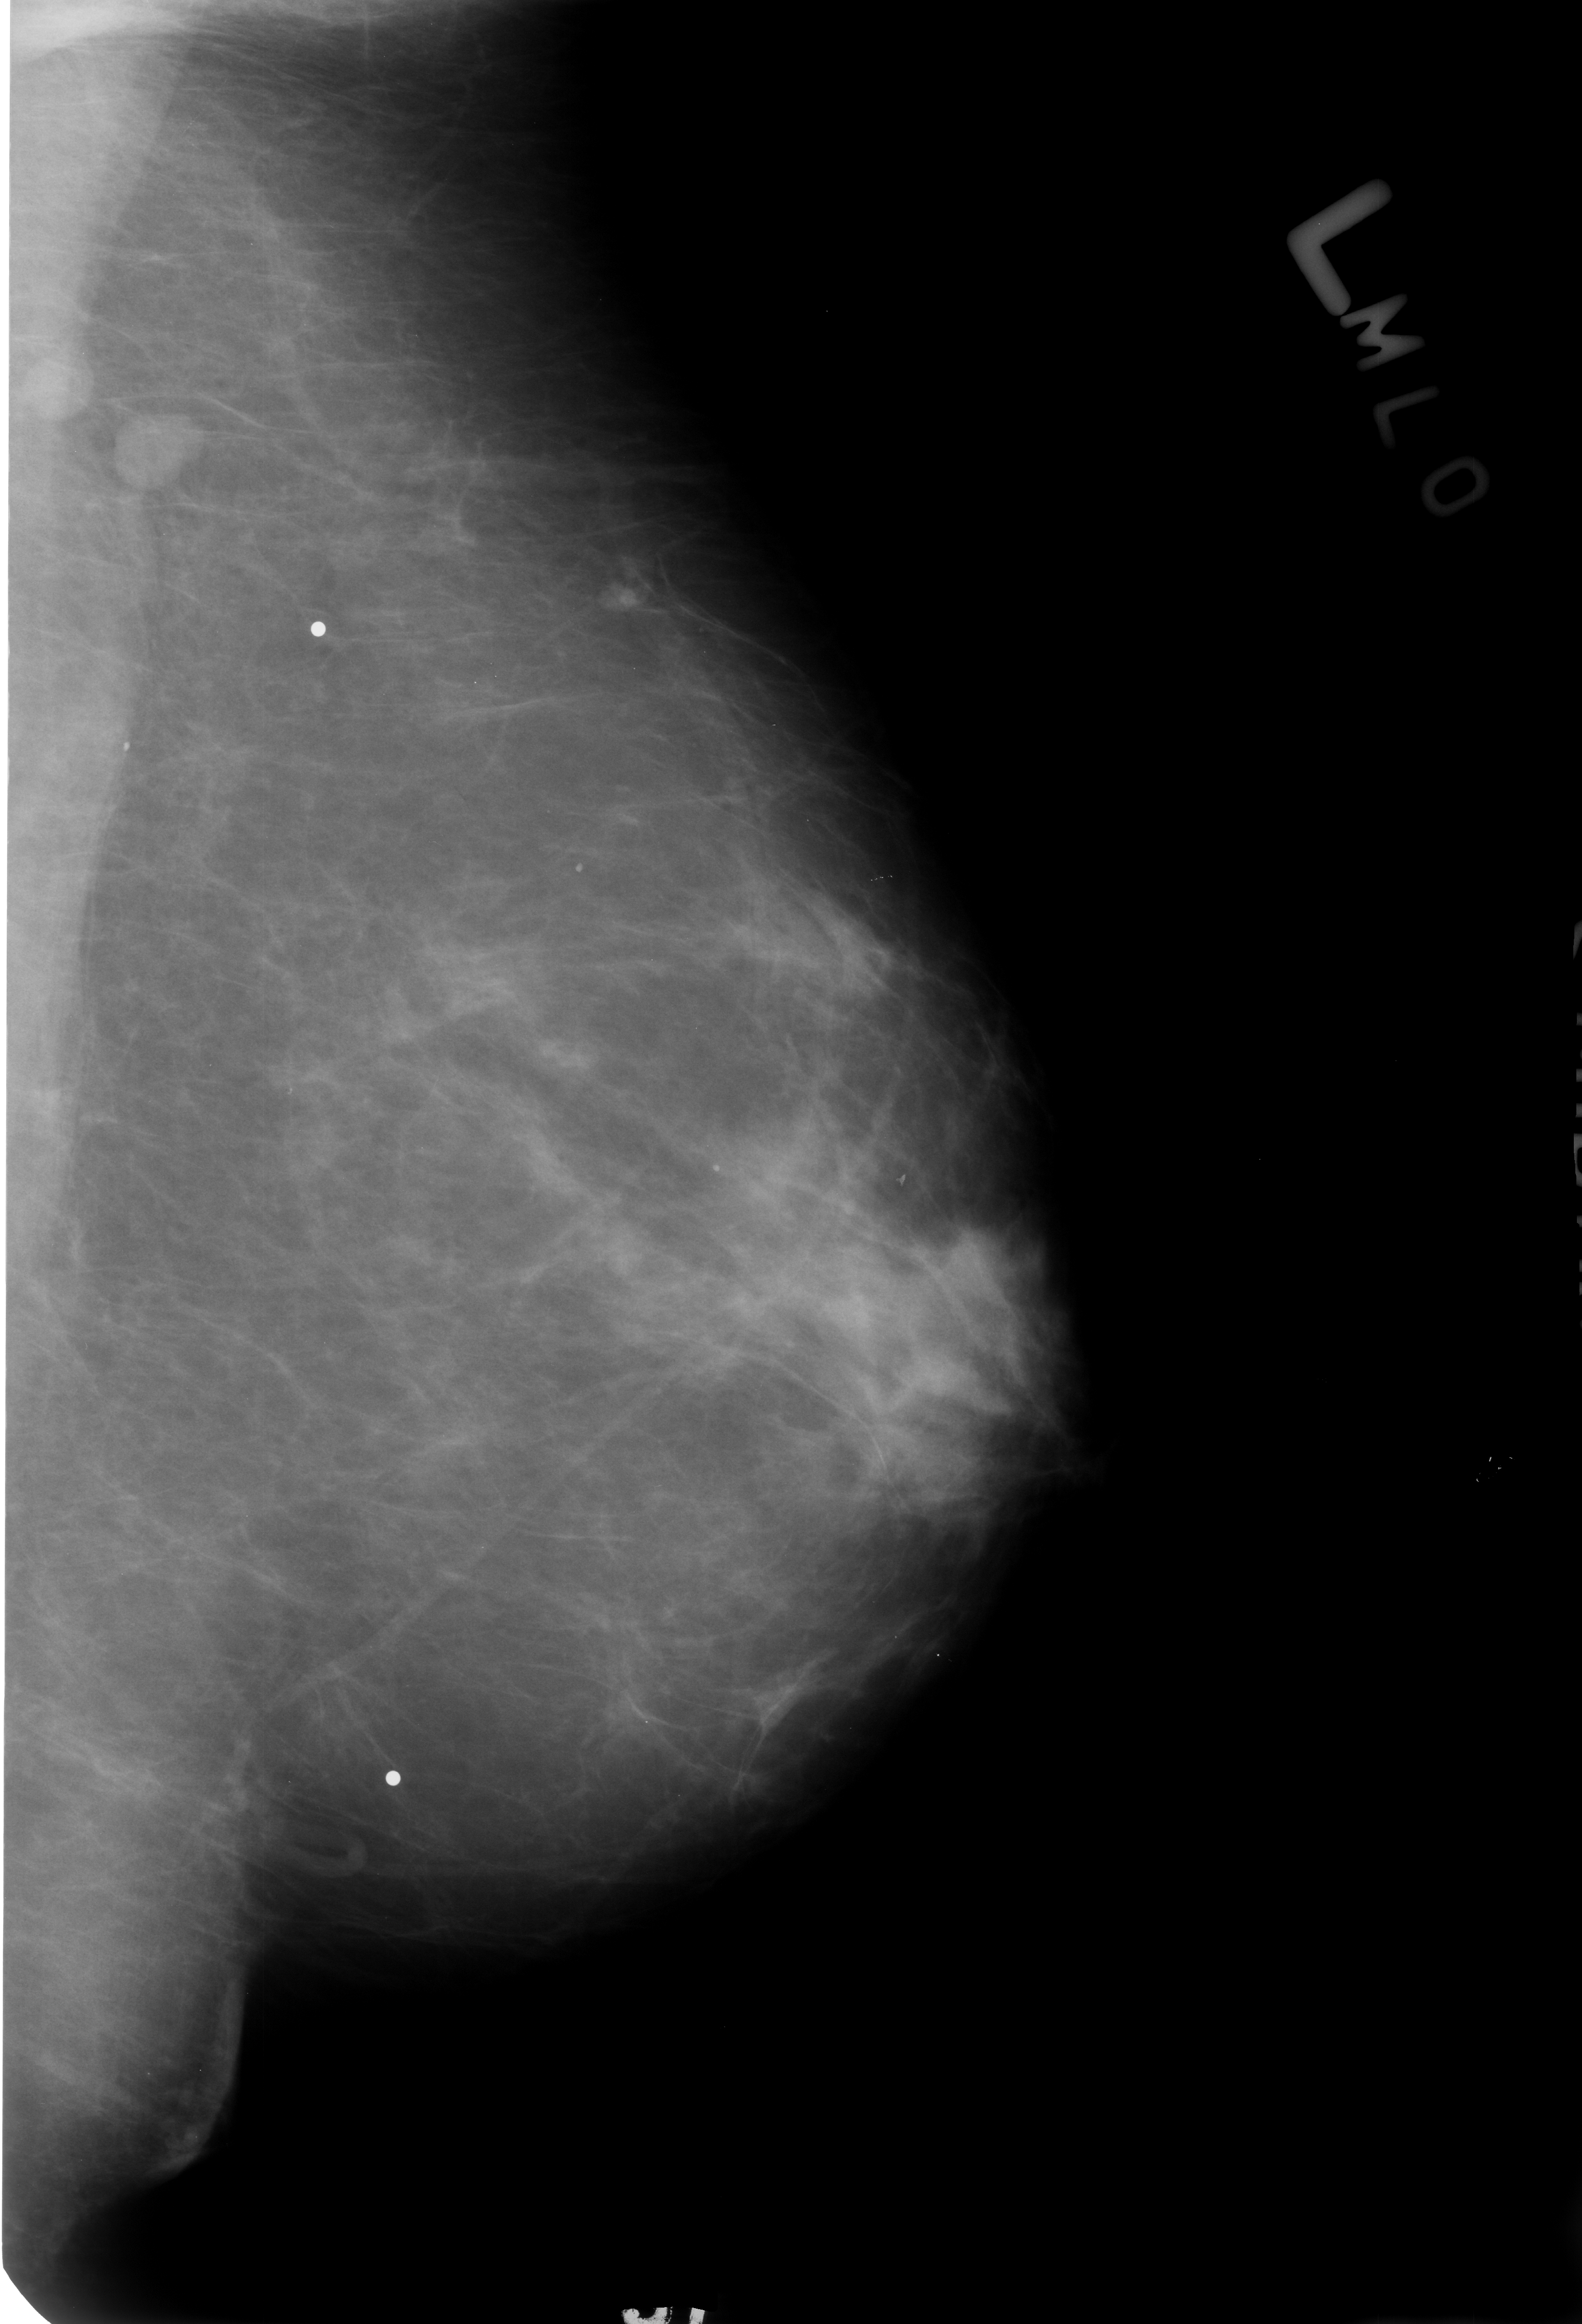
Scanned film-screen mammogram; left breast; MLO view; BI-RADS breast density category 2 (scale 1–4).
Marked findings (only marked abnormalities are described; nothing is implied about the rest of the image): Finding 1 of 3: calcifications, morphology punctate; BI-RADS assessment category 2; benign without callback (not worked up further). Finding 2 of 3: calcifications, morphology punctate; BI-RADS assessment category 2; subtlety rating 3 on a 1 (subtle) to 5 (obvious) scale; benign without callback (not worked up further). Finding 3 of 3: calcifications, morphology punctate; BI-RADS assessment category 2; subtlety rating 3 on a 1 (subtle) to 5 (obvious) scale; benign without callback (not worked up further).